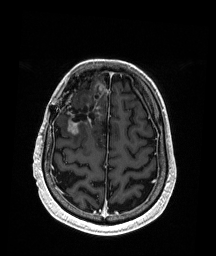
Brain MRI from a brain-tumour surgery series, one axial slice; slice 51 of 192 in the series (ordered by position); T1-weighted post-contrast; 216 × 256 image matrix, field of view 211 × 250 mm. Case-level facts recorded for this patient, not image findings: histopathology: Astrocytoma; WHO grade: 3; IDH mutation: yes; tumour location: Right Frontal.
Outlined on this slice (expert manual segmentation):
- previous resection cavity: box from (x=64, y=95) to (x=100, y=126) px
- tumour: (x=68, y=85)–(x=107, y=135)